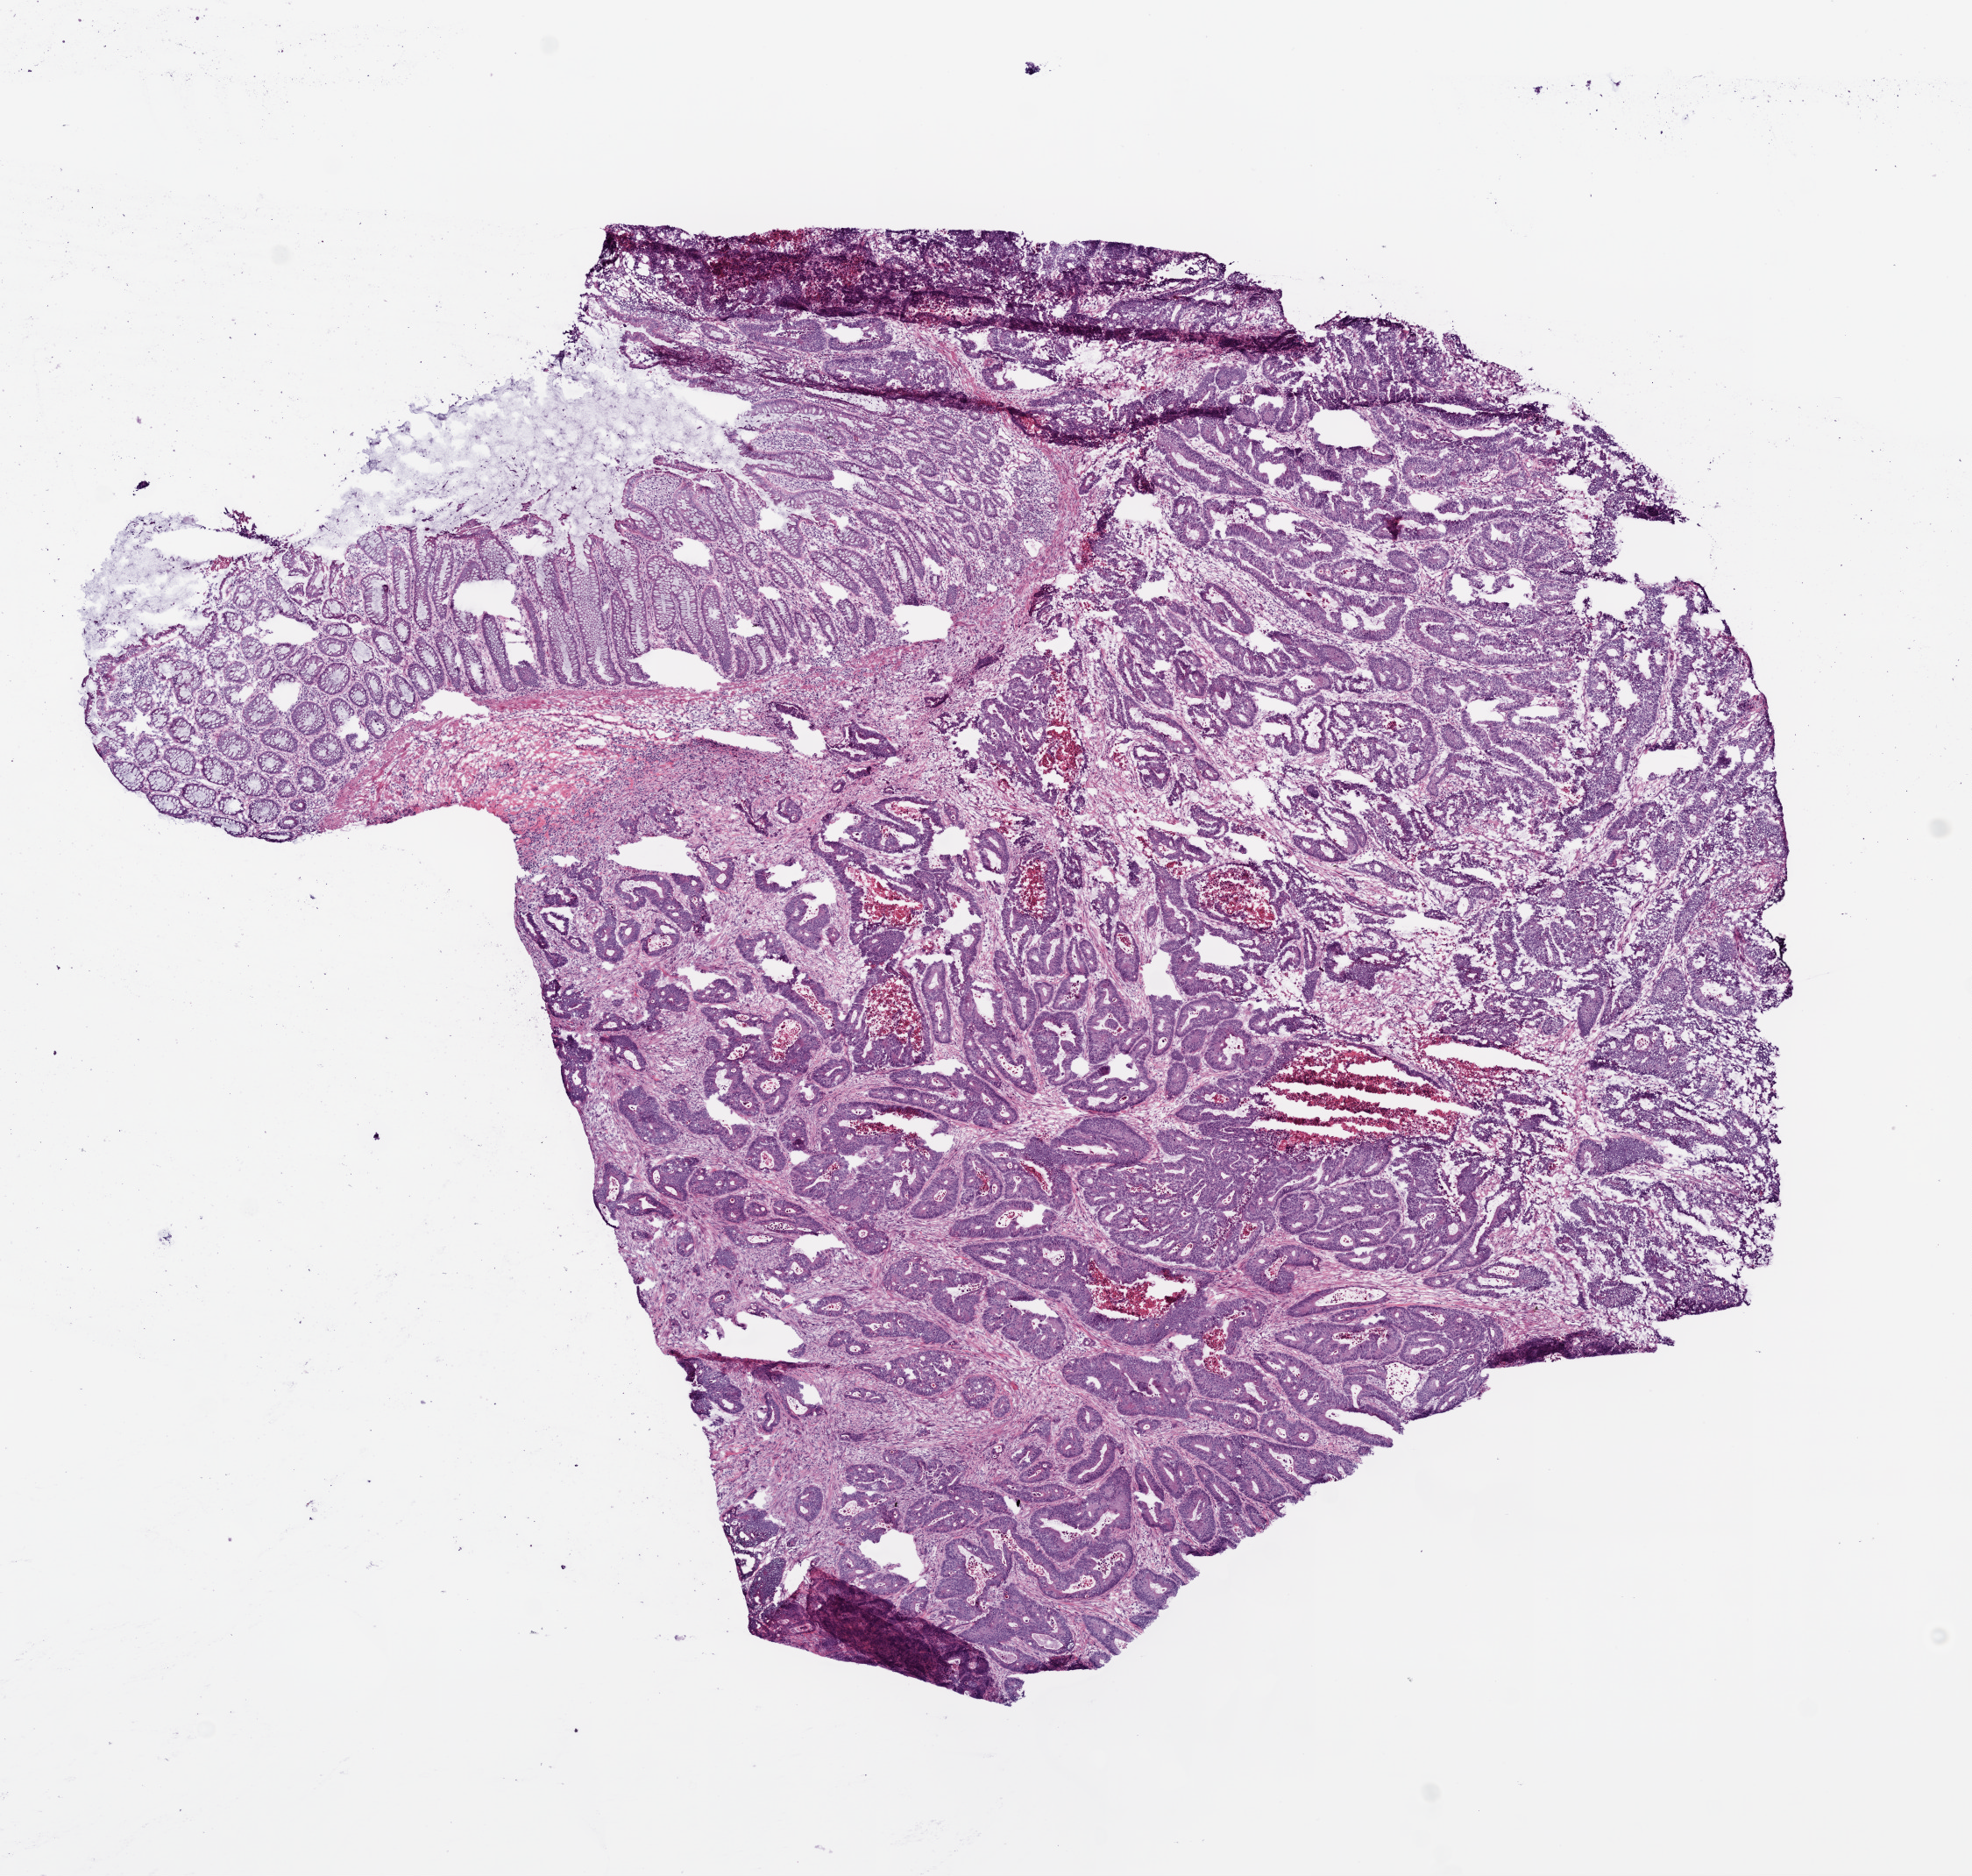
Digitized H&E-stained tissue section (whole slide), low-resolution overview of the scanned area, about 9.0 x 8.6 mm, frozen section from the bottom of the tissue portion, rectum, primary tumour sample. Female patient; age at initial diagnosis 84 years. Composition of this section per pathologist review: tumour cells 57%, tumour nuclei 75%, normal cells 25%, stromal cells 10%, necrosis 8%.
- AJCC pathologic stage: I (6th edition)
- pathologic diagnosis: Adenocarcinoma, NOS
- lymph nodes positive (case pathology): 0 of 12 examined